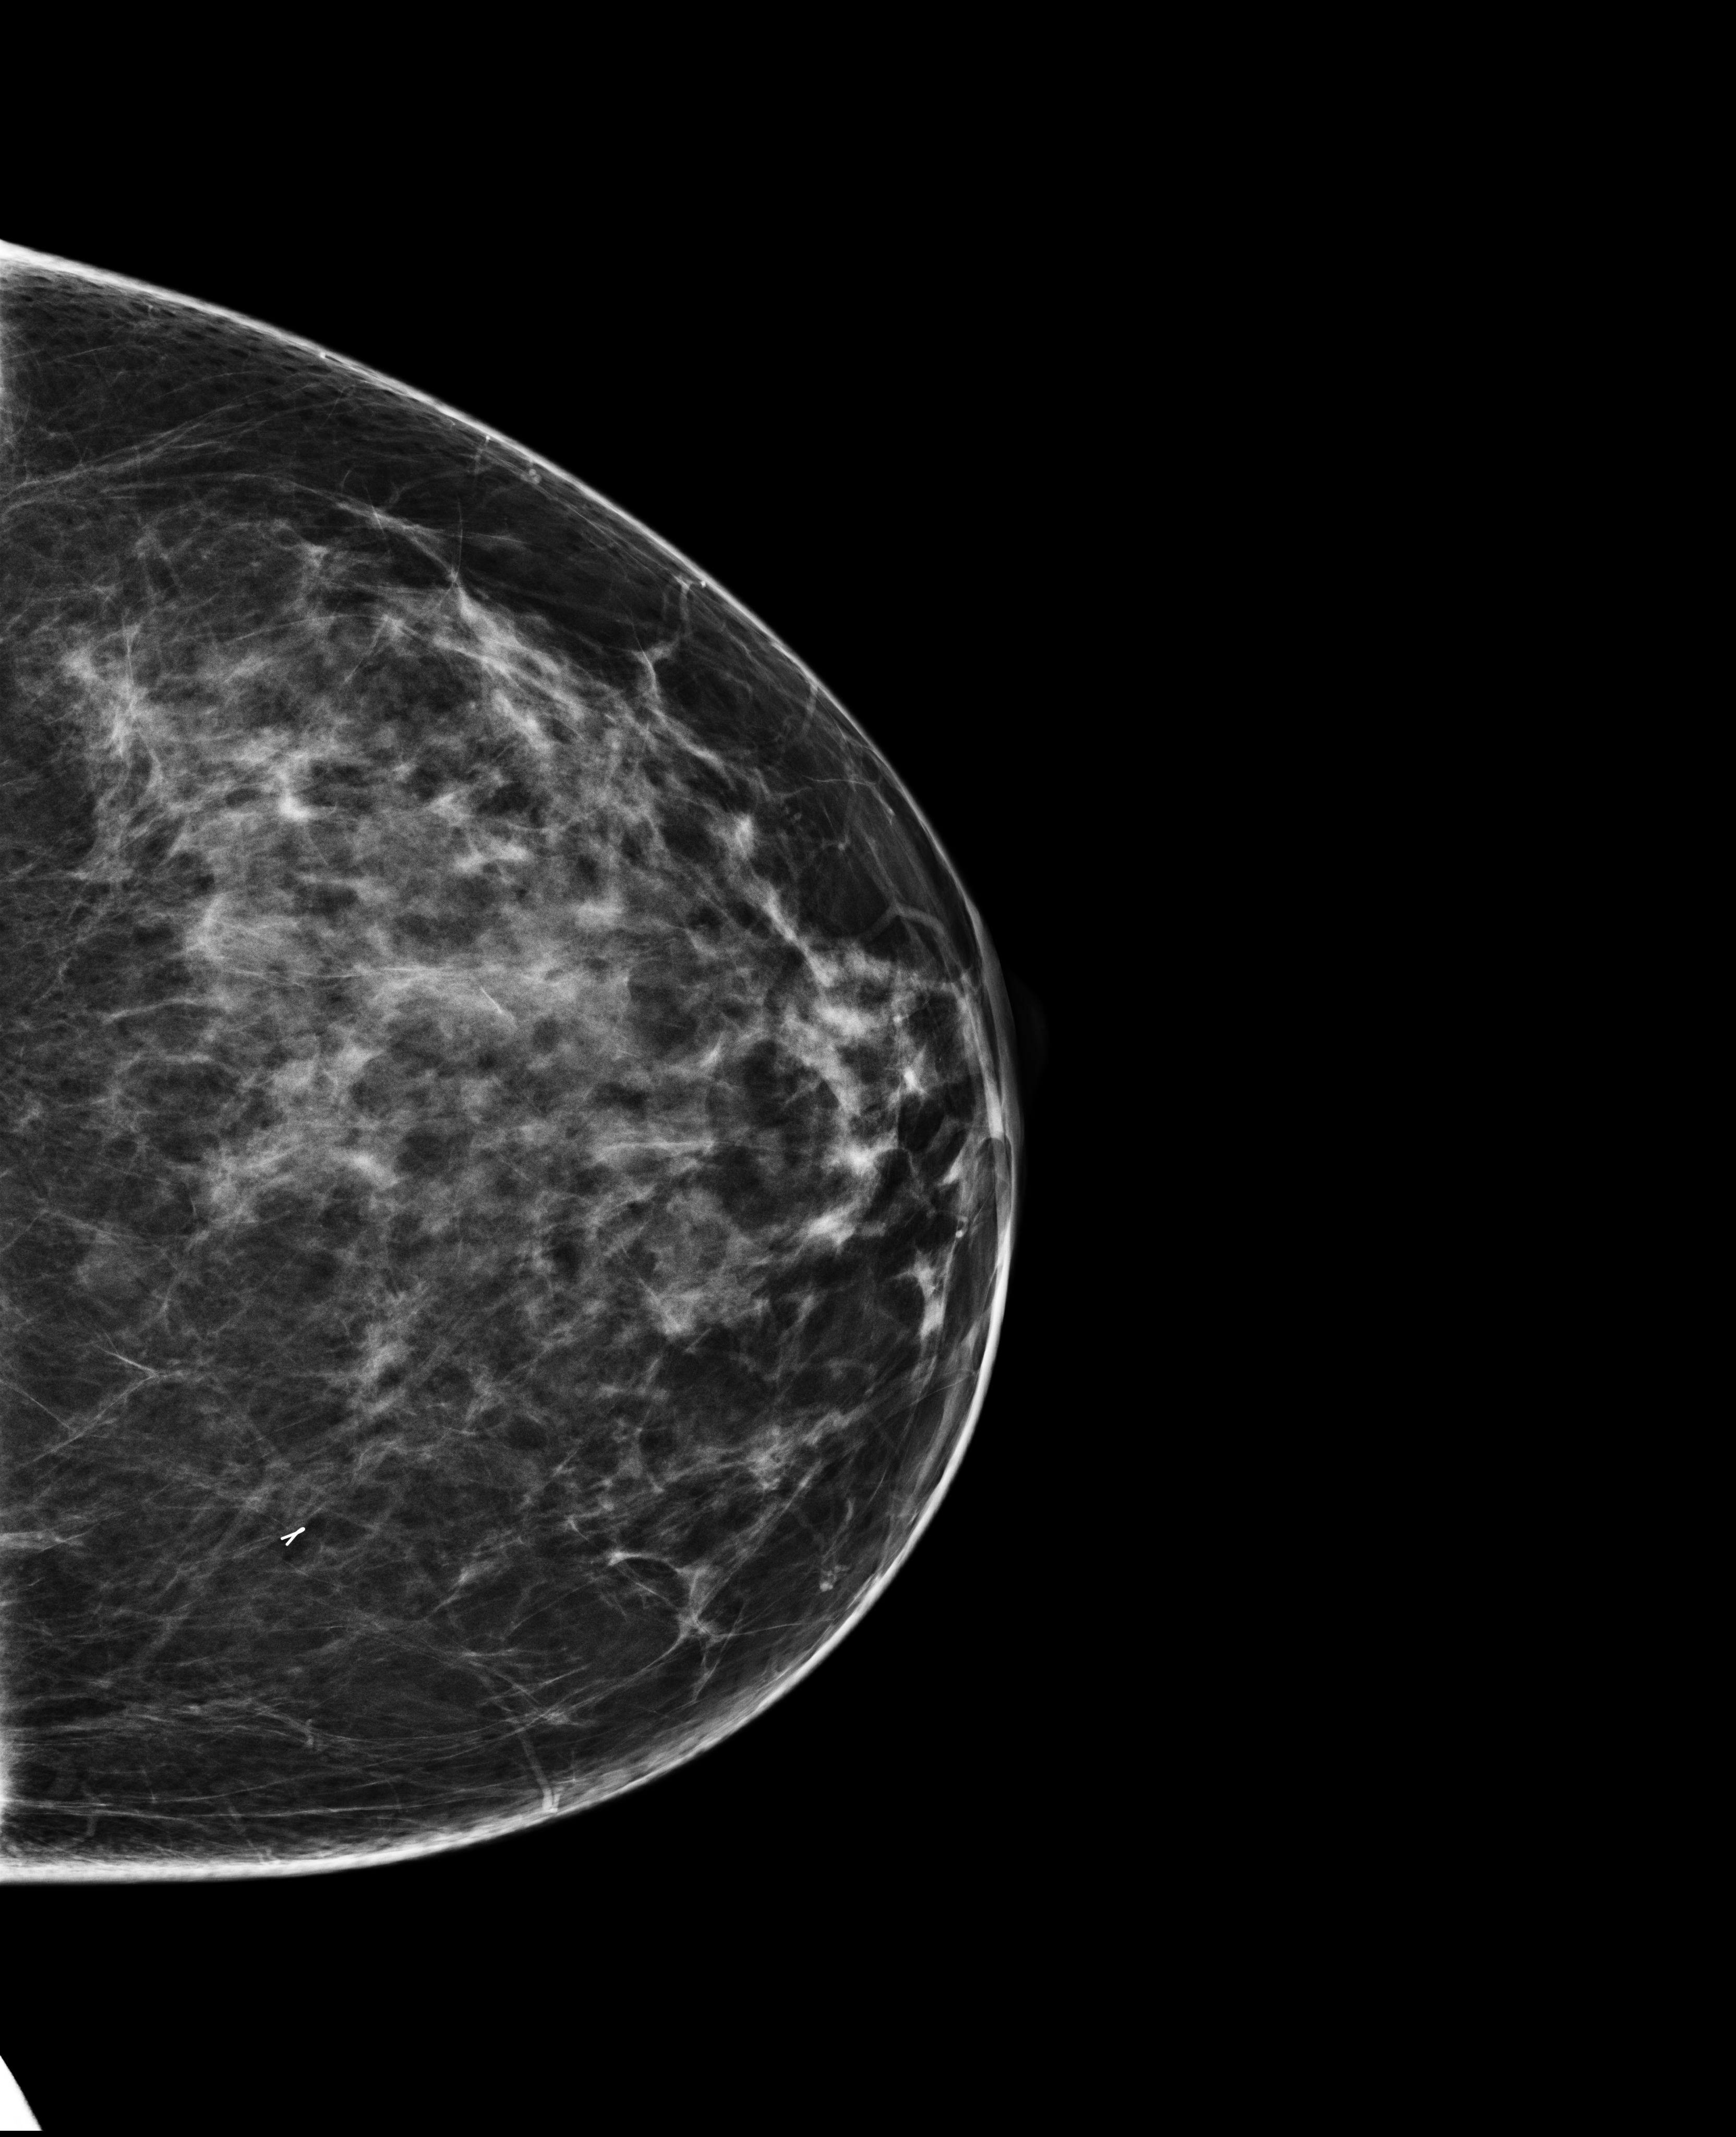
Full-field digital mammogram (FFDM); left breast; cranio-caudal projection; annual screening mammography examination; compressed breast thickness 75 mm; system: Selenia Dimensions. Female patient, age 50 years.
BI-RADS breast density category at the screening exam (both breasts, scale 1–4): 3. Final BI-RADS category for the screening round (tomosynthesis exam, both breasts): category 1. Recall: no recall after this screen.